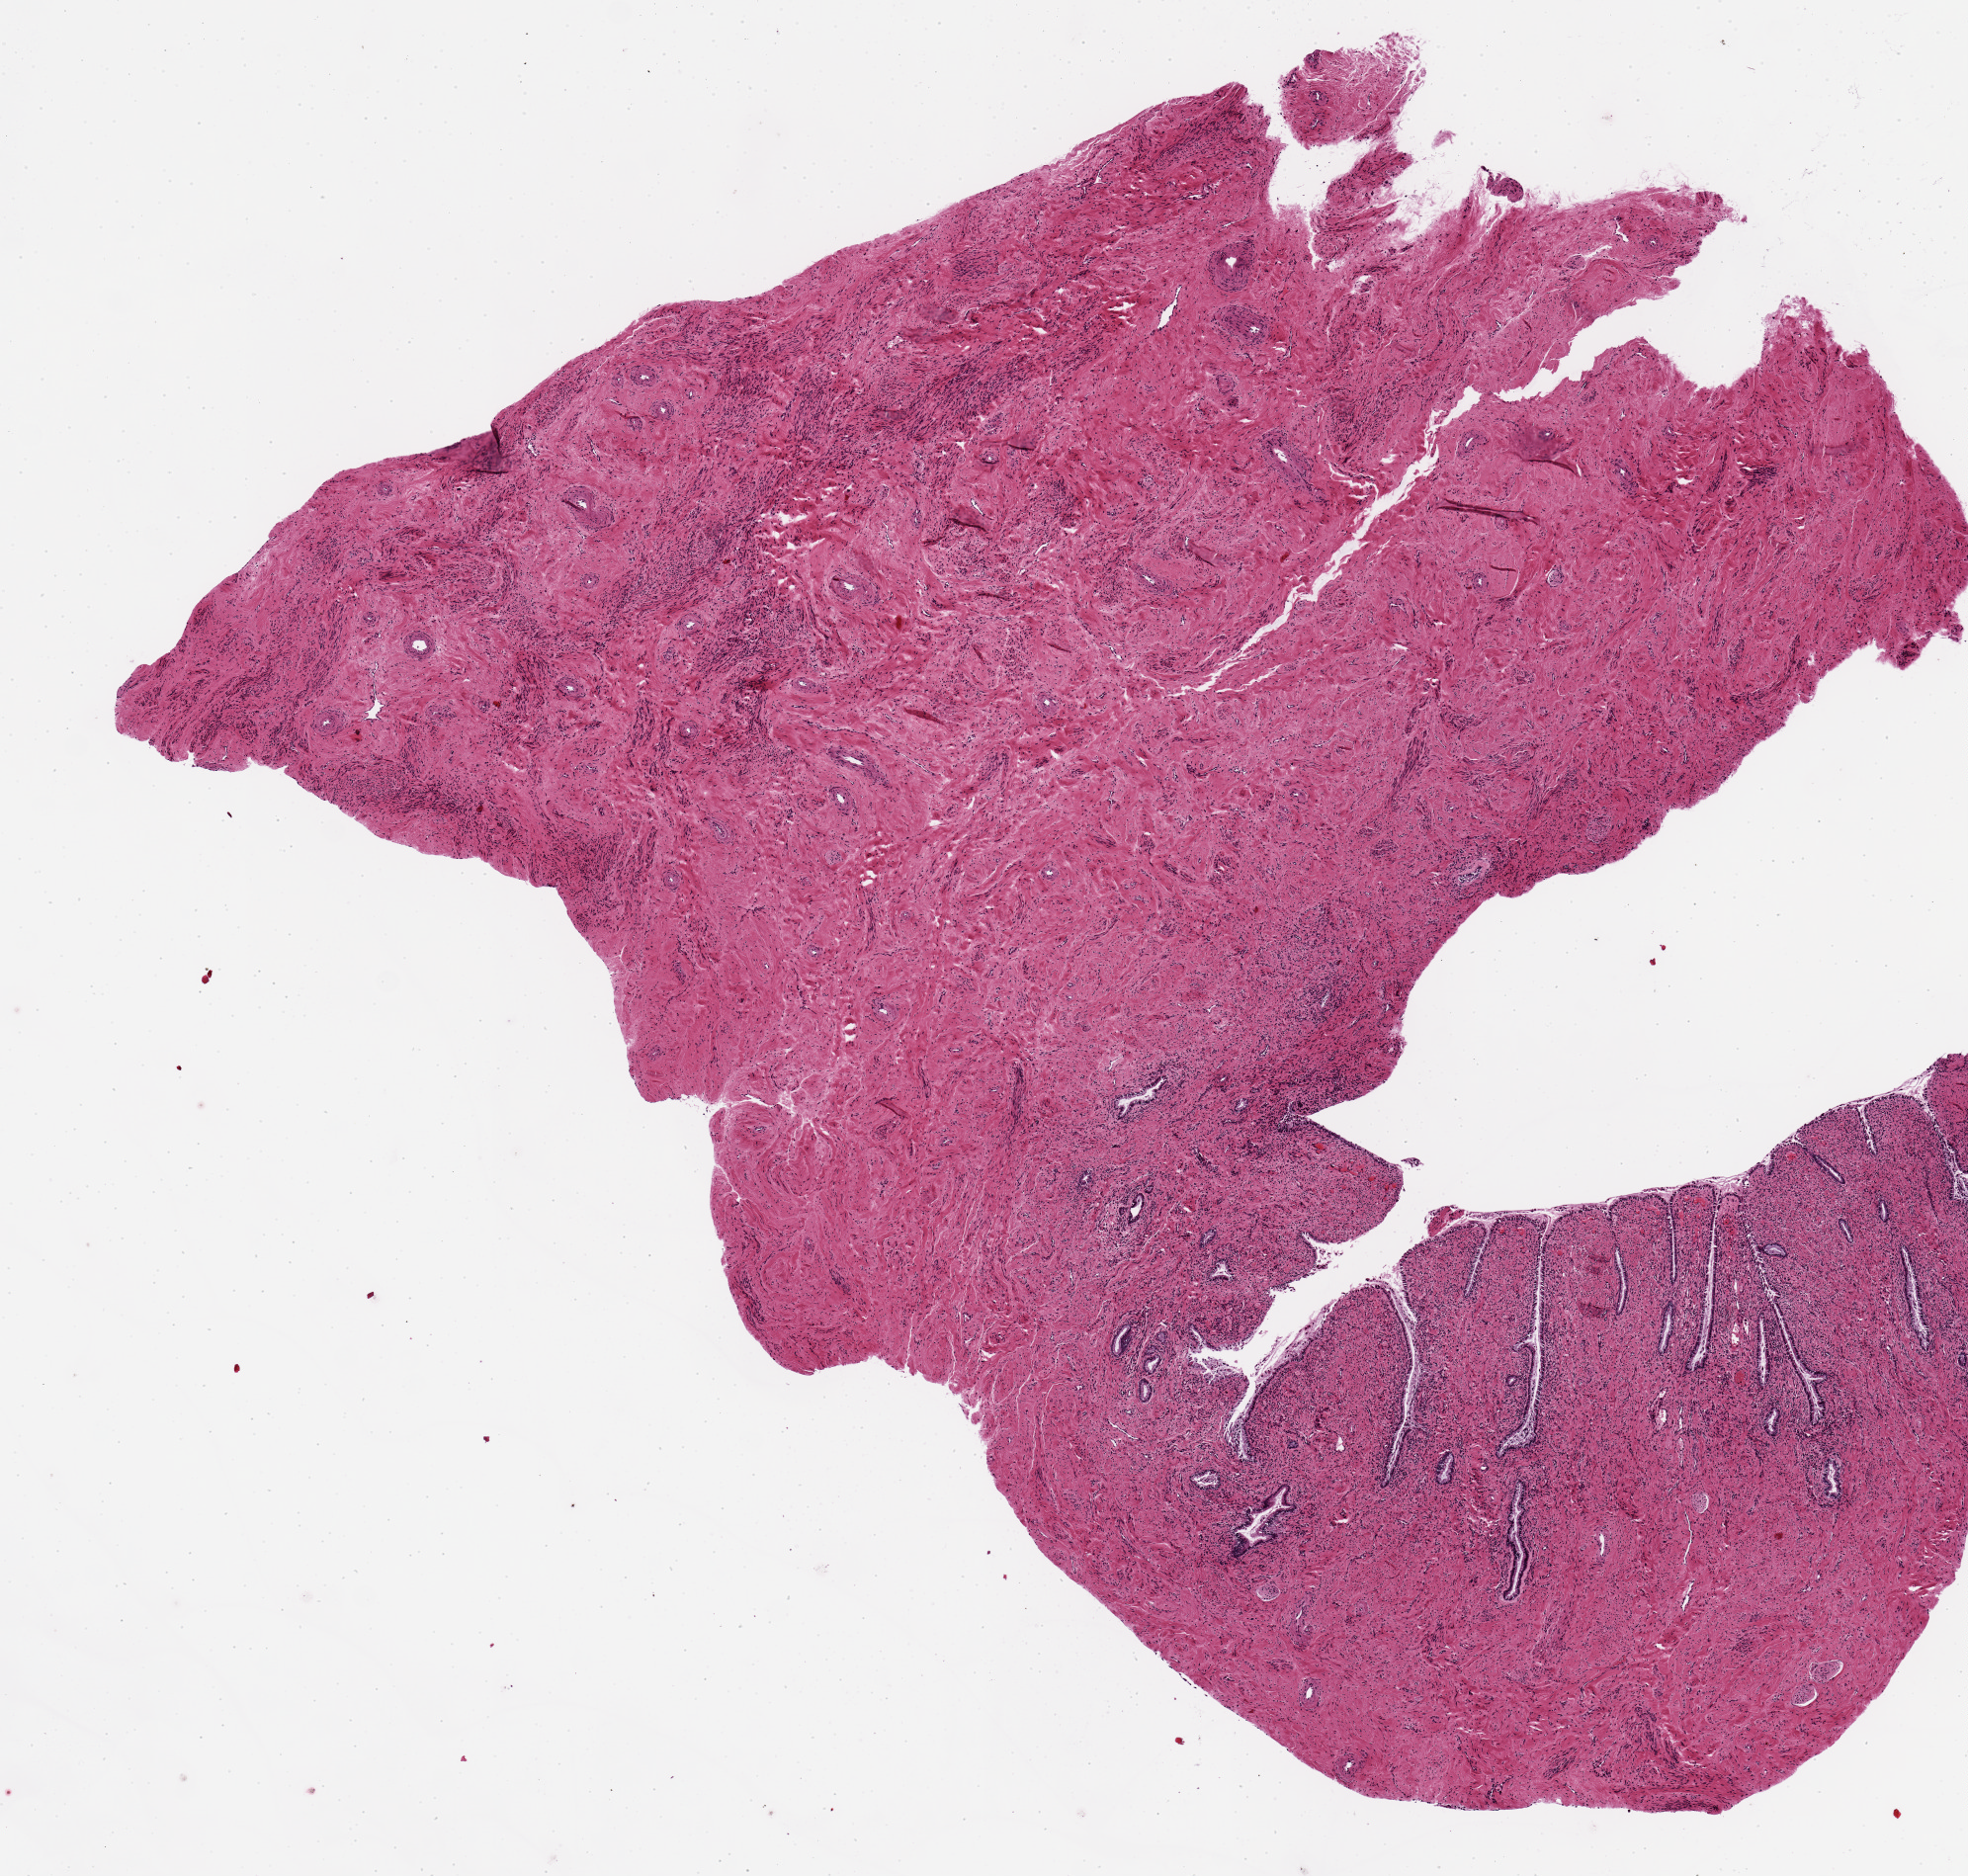
Hematoxylin and eosin (H&E) whole-slide image — whole scanned area (about 7.9 x 7.5 mm) shown as a low-resolution overview; PAXgene-fixed, paraffin-embedded tissue; section of endocervix (target tissue); donor tissue sample. Donor: female.
Reviewer comment on this tissue sample: Epithelium is present, beginning to slough.